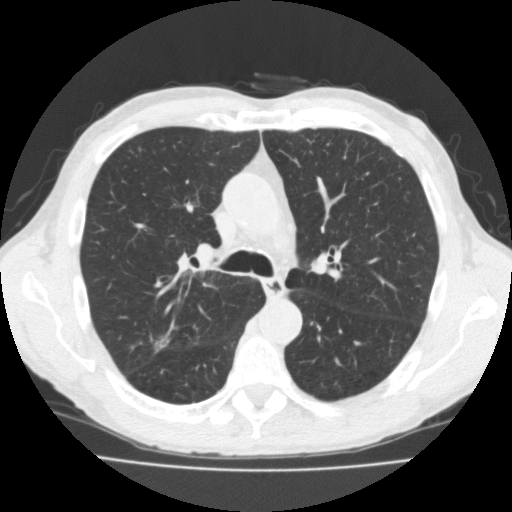
Low-dose screening chest CT, one axial slice. Reconstruction kernel FC10. Lung window (W 1500 / L -600 HU). 2 mm slice thickness. 512 × 512 image matrix.
Annotated regions visible in this slice (manually delineated by an expert):
- lesion 1 (tumor, upper lobe of right lung): bounding box <154,338,169,353> (left, top, right, bottom; pixels)